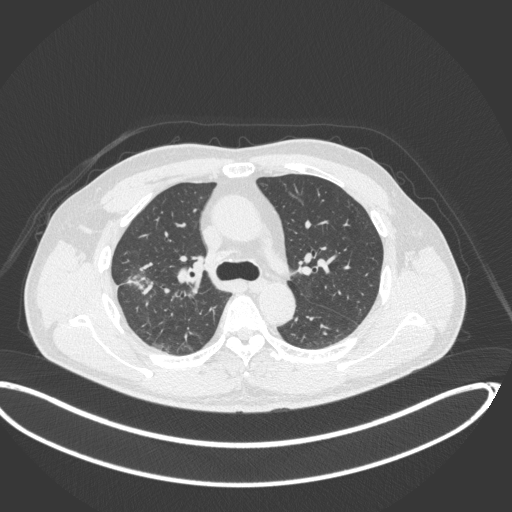
Chest CT, one axial slice. Position 227 of 341 along the scan axis. Reconstruction kernel B31f. 120 kVp. Lung window (W 1500 / L -600 HU). 1 mm slice thickness. 512 × 512 image matrix. Male patient, age 63 years. From the clinical record (not read from this slice): clinical TNM (as recorded): T1c N0 M0; histopathological grade: G2-3.
Structures marked on this image (rectangle marked by the reading radiologist):
- lung tumour (recorded histology: adenocarcinoma): bounding box <125,258,157,296> (left, top, right, bottom; pixels)